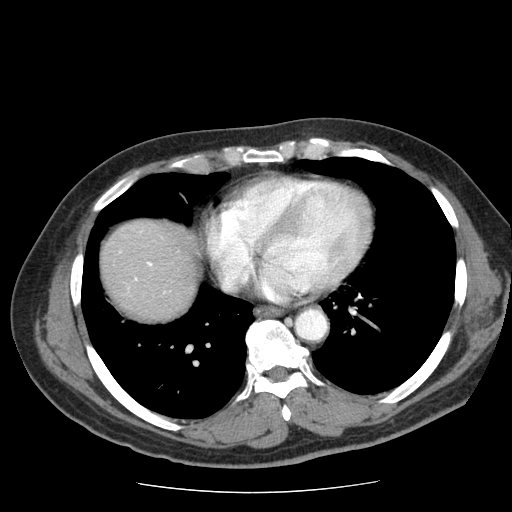
Contrast-enhanced abdominal CT (liver protocol), one axial slice; position 72 of 85 along the scan axis; reconstruction kernel STANDARD; soft-tissue window (W 400 / L 40 HU); 2.5 mm slice thickness; 512 × 512 image matrix, field of view 360 × 360 mm. From the clinical record (not read from this slice): diagnosis: hepatocellular carcinoma (patient treated with transarterial chemoembolisation; whether this scan precedes or follows treatment is not stated here); TNM stage (as recorded): Stage-IIIA; Child-Pugh class: A.
Structures marked on this image (semi-automatic segmentation, software-assisted and operator-edited):
- liver parenchyma outside the tumour (the mass and vessels are separate outlines, so this box may not span the whole liver): box from (x=102, y=220) to (x=198, y=320) px
- liver vessels: (x=136, y=262)–(x=152, y=280)